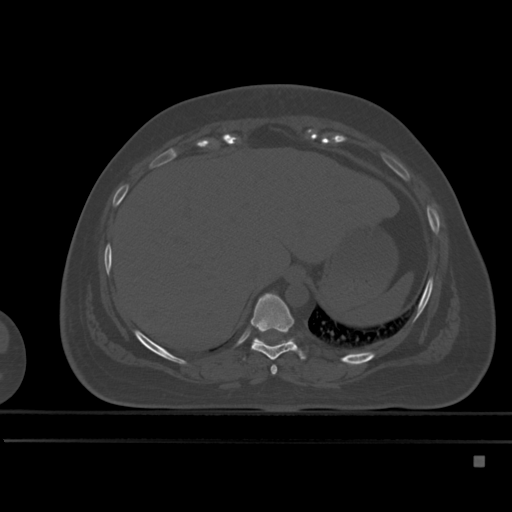
CT including the spine, one axial slice; position 260 of 495 along the scan axis; bone window (W 1800 / L 400 HU); 1.5 mm slice thickness; 512 × 512 image matrix. Patient: female, 33 years. From the clinical record (not read from this slice): primary cancer: breast; vertebrae with lytic lesions (as recorded): T1.
Annotated regions visible in this slice (semi-automatic segmentation, software-assisted and operator-edited):
- T10 vertebra: bounding box <252,337,294,345> (left, top, right, bottom; pixels)
- T8 vertebra: <271,365,277,375>
- T9 vertebra: <250,293,306,360>